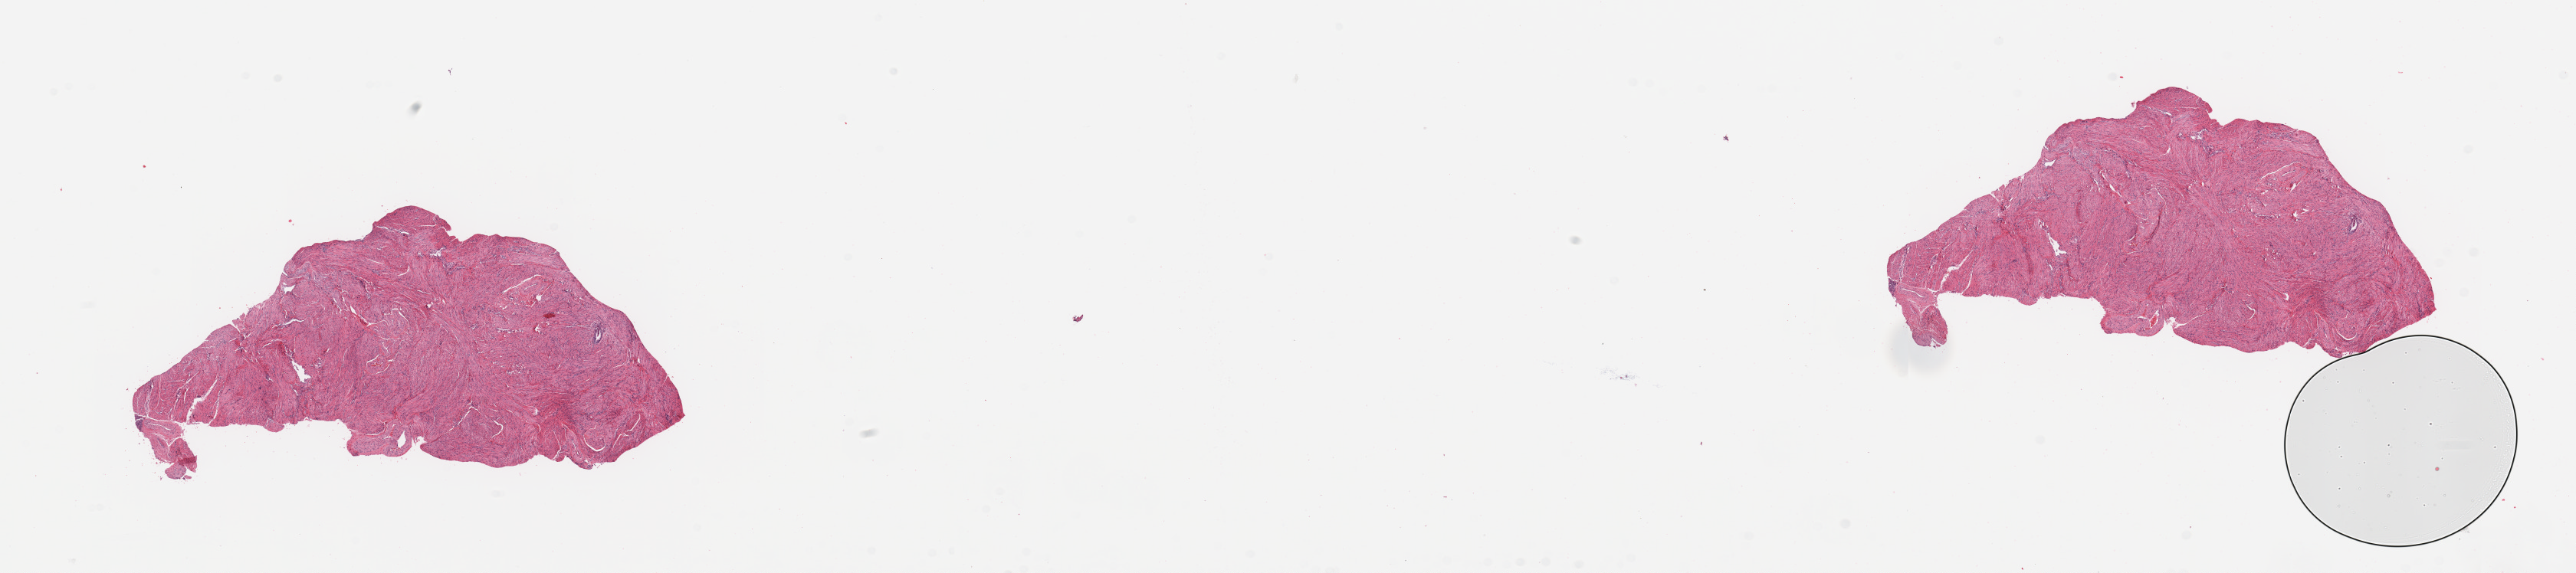
Digitized H&E tissue section (whole slide), whole scanned area (about 26.6 x 5.9 mm, from a 20x scan) shown as a low-resolution overview. Uterus, normal (non-tumour) tissue. Patient: female, age 61 years.
This section: normal (non-tumour) tissue from the same patient. Patient diagnosis: Endometrioid adenocarcinoma, NOS.